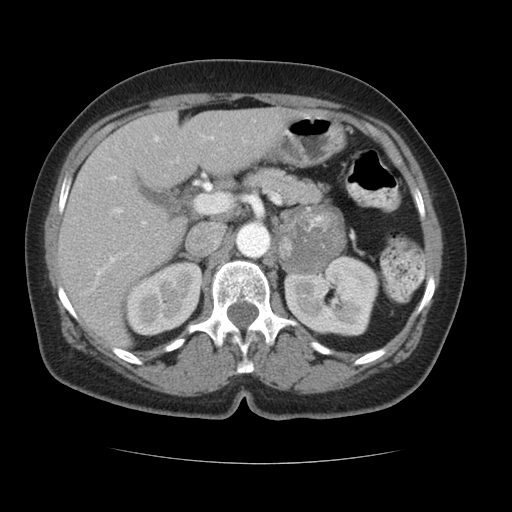
Contrast-enhanced abdominal CT, one axial slice. Position 65 of 96 along the scan axis. Reconstruction kernel STANDARD. Intravenous contrast given. Soft-tissue window (W 400 / L 40 HU). 512 × 512 image matrix. Female patient, age 66 years. Case-level facts recorded for this patient, not image findings: diagnosis: adrenocortical carcinoma; tumour side: left adrenal; tumour size at pathology: 5.5 cm; Ki-67 index: 15 %; stage (as recorded): 3.
Structures marked on this image (semi-automatically segmented with operator editing):
- mass: box from (x=280, y=207) to (x=345, y=271) px